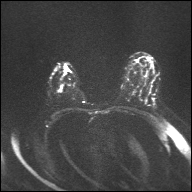
Breast MRI, one axial slice; diffusion-weighted series; image 2 of 4 stored at this slice position (different b-values; order by instance number); 1.5 T; 192 × 192 image matrix. Female patient.
Outlined on this slice (outlined manually by an expert reader):
- tumour on diffusion-weighted imaging: box from (x=59, y=85) to (x=62, y=91) px